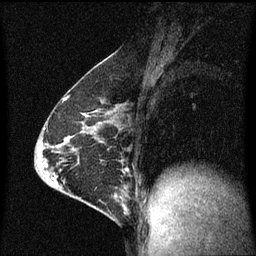
Breast MRI (dynamic contrast-enhanced), one sagittal slice; slice 36 of 60 in the series (ordered by position); dynamic contrast-enhanced series, image 2 of 3 at this slice position (ordered by acquisition); 1.5 T; TE 4.2 ms, TR 8 ms; 2 mm slice thickness; 256 × 256 image matrix. Patient: female, 64 years.
Structures marked on this image (semi-automatically segmented with operator editing):
- analysis volume of interest (the breast-tissue region the enhancement analysis was run in; not a lesion): bounding box <87,182,130,217> (left, top, right, bottom; pixels)
- tumour enhancement mask (voxels above the 70 % enhancement threshold inside the analysis volume of interest): <94,196,126,211>